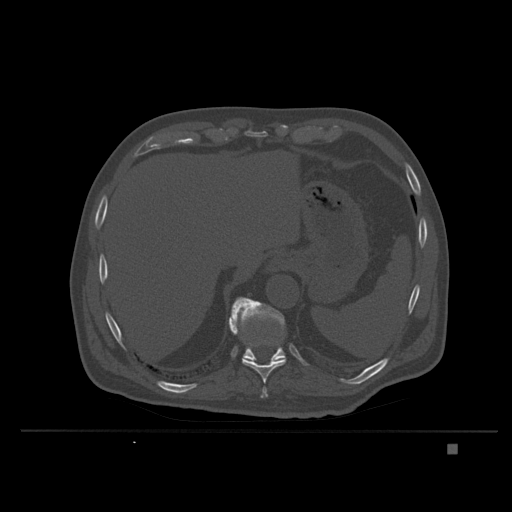
CT including the spine, one axial slice; slice 189 of 435 in the series (ordered by position); bone window (W 1800 / L 400 HU); 1.5 mm slice thickness; 512 × 512 image matrix, field of view 434 × 434 mm. Patient: male, 73 years. Case-level facts recorded for this patient, not image findings: primary cancer: skin.
Outlined on this slice (semi-automatically segmented with operator editing):
- T10 vertebra: box from (x=229, y=324) to (x=286, y=384) px
- T11 vertebra: (x=229, y=297)–(x=286, y=363)
- T9 vertebra: (x=261, y=387)–(x=268, y=398)